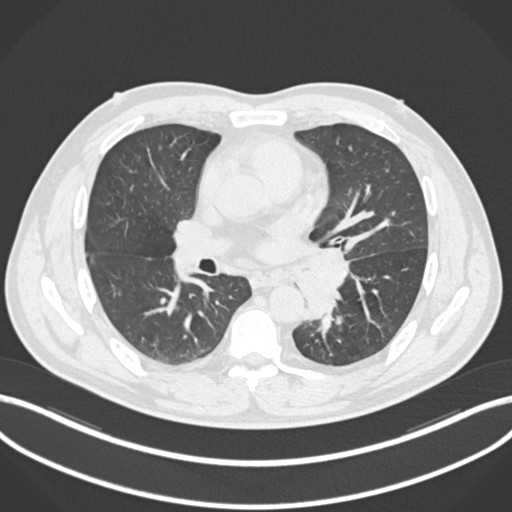
Chest CT, one axial slice. Position 120 of 223 along the scan axis. Lung window (W 1500 / L -600 HU). 1 mm slice thickness. 512 × 512 image matrix, field of view 400 × 400 mm. Male patient, age 50 years. Case-level facts recorded for this patient, not image findings: clinical TNM (as recorded): T2a N3 M0.
Structures marked on this image (rectangle marked by the reading radiologist):
- lung tumour (recorded histology: squamous cell carcinoma): bounding box <293,243,348,324> (left, top, right, bottom; pixels)